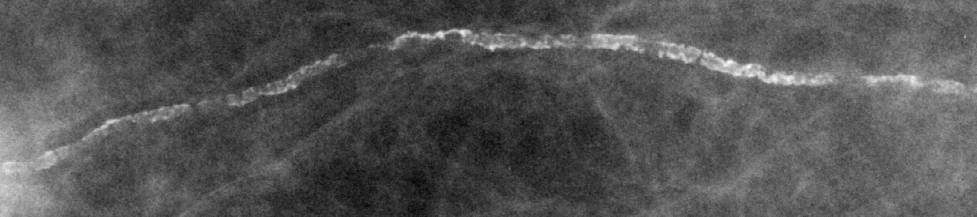
Cropped region of a digitized screen-film mammogram centred on a radiologist-marked abnormality; right breast; CC view.
Marked abnormality: calcifications, morphology vascular; BI-RADS assessment category 2; benign; no additional work-up was recommended (benign without callback).